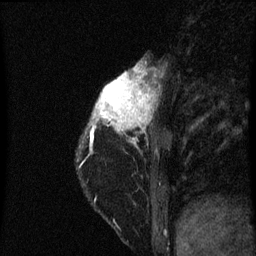
Breast MRI (dynamic contrast-enhanced), one sagittal slice; slice 16 of 60 in the series (ordered by position); dynamic contrast-enhanced series, image 2 of 3 at this slice position (ordered by acquisition); 1.5 T; TE 4.2 ms, TR 8 ms; 2 mm slice thickness; 256 × 256 image matrix. Patient: female, 38 years.
Structures marked on this image (semi-automatic segmentation, software-assisted and operator-edited):
- analysis volume of interest (the breast-tissue region the enhancement analysis was run in; not a lesion): bounding box [x1, y1, x2, y2] px = [82, 66, 159, 141]
- tumour enhancement mask (voxels above the 70 % enhancement threshold inside the analysis volume of interest): [92, 66, 151, 131]